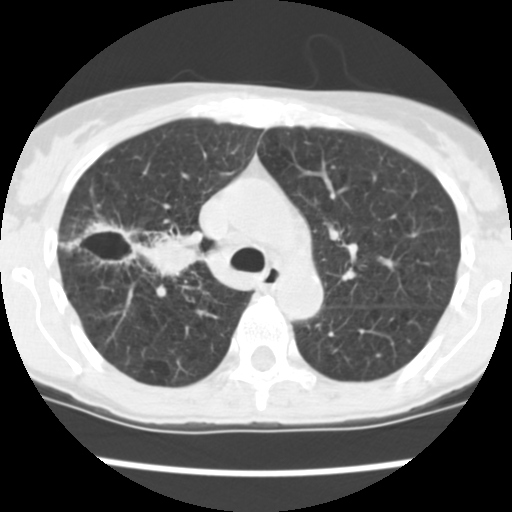
Low-dose screening chest CT, one axial slice. Slice 169 of 252 in the series (ordered by position). Reconstruction kernel STANDARD. 120 kVp. Lung window (W 1500 / L -600 HU). 2.5 mm slice thickness. 512 × 512 image matrix, field of view 276 × 276 mm.
Structures marked on this image (manually delineated by an expert):
- lesion 2 (tumor, lower lobe of right lung): bounding box [x1, y1, x2, y2] px = [83, 219, 203, 277]